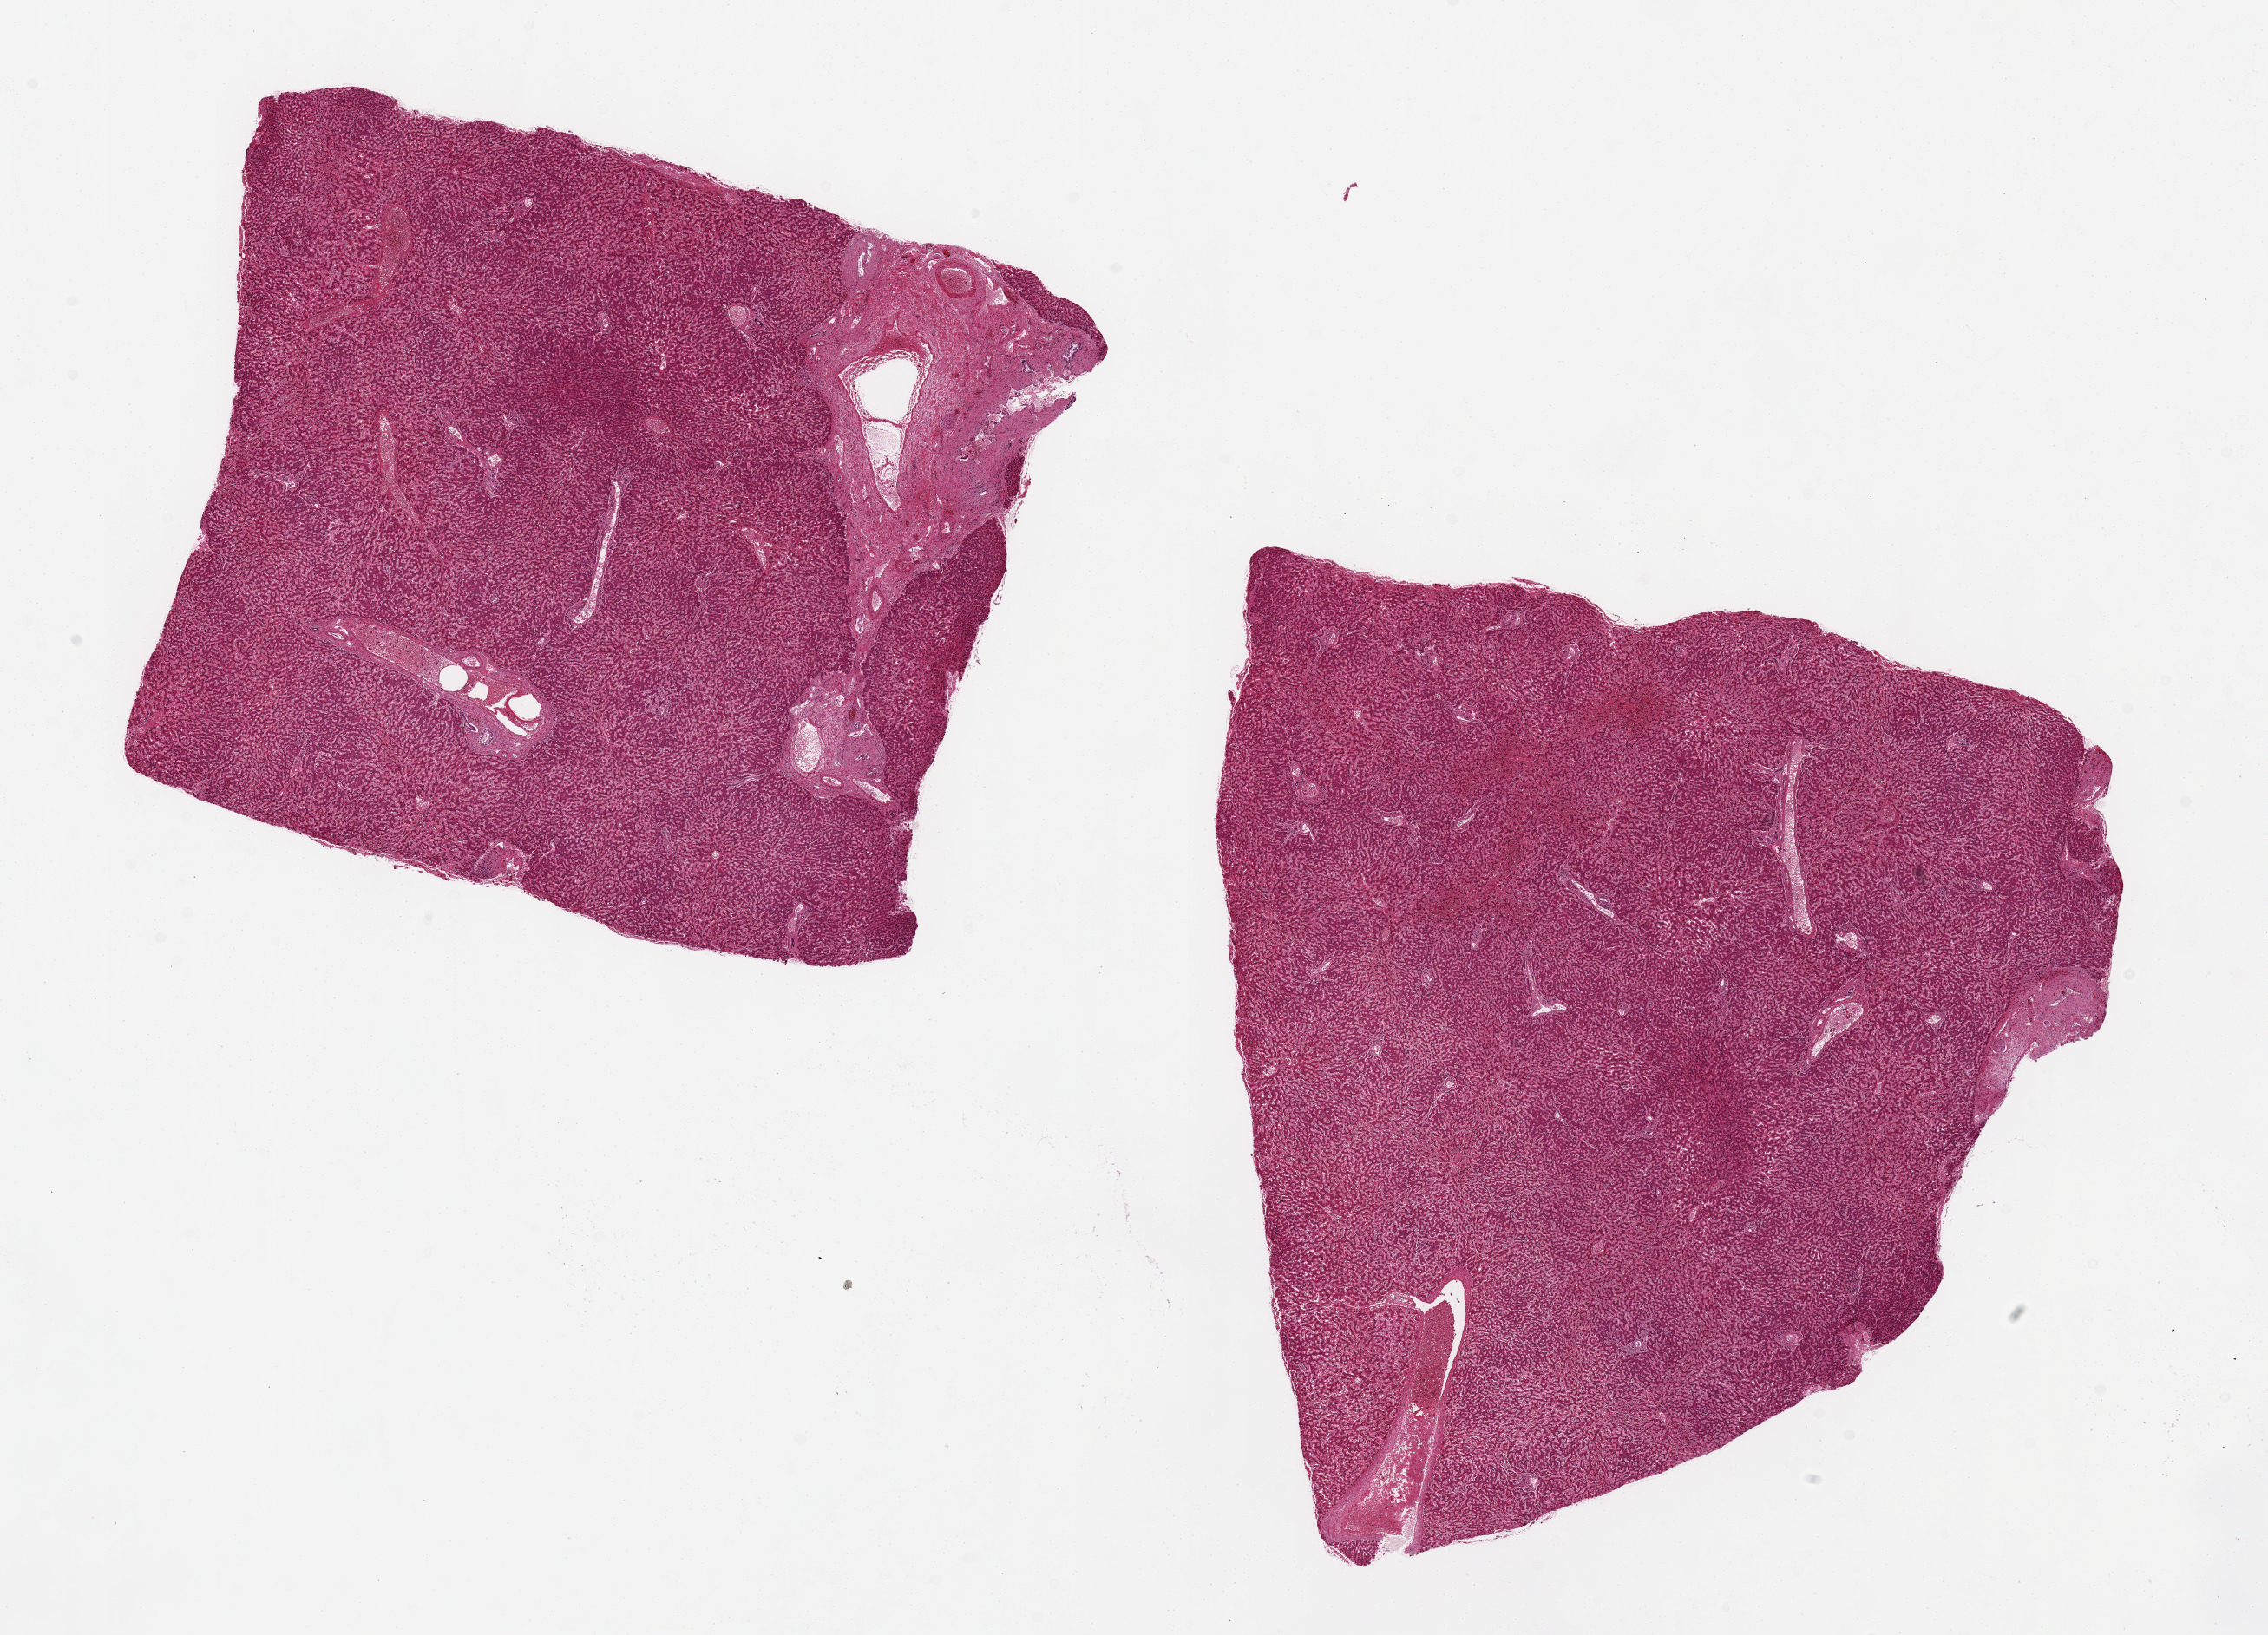
Digitized H&E-stained section — low-resolution overview of the scanned area, about 20.7 x 14.9 mm (slide scanned at 20x); PAXgene-fixed paraffin-embedded (PFPE) section; section of liver (target tissue); tissue donor sample. Donor sex: female.
• pathologist's review note for this sample: 2 pieces 9x8 & 8x7 mm; centrally congested and moderately autolyzed centrally